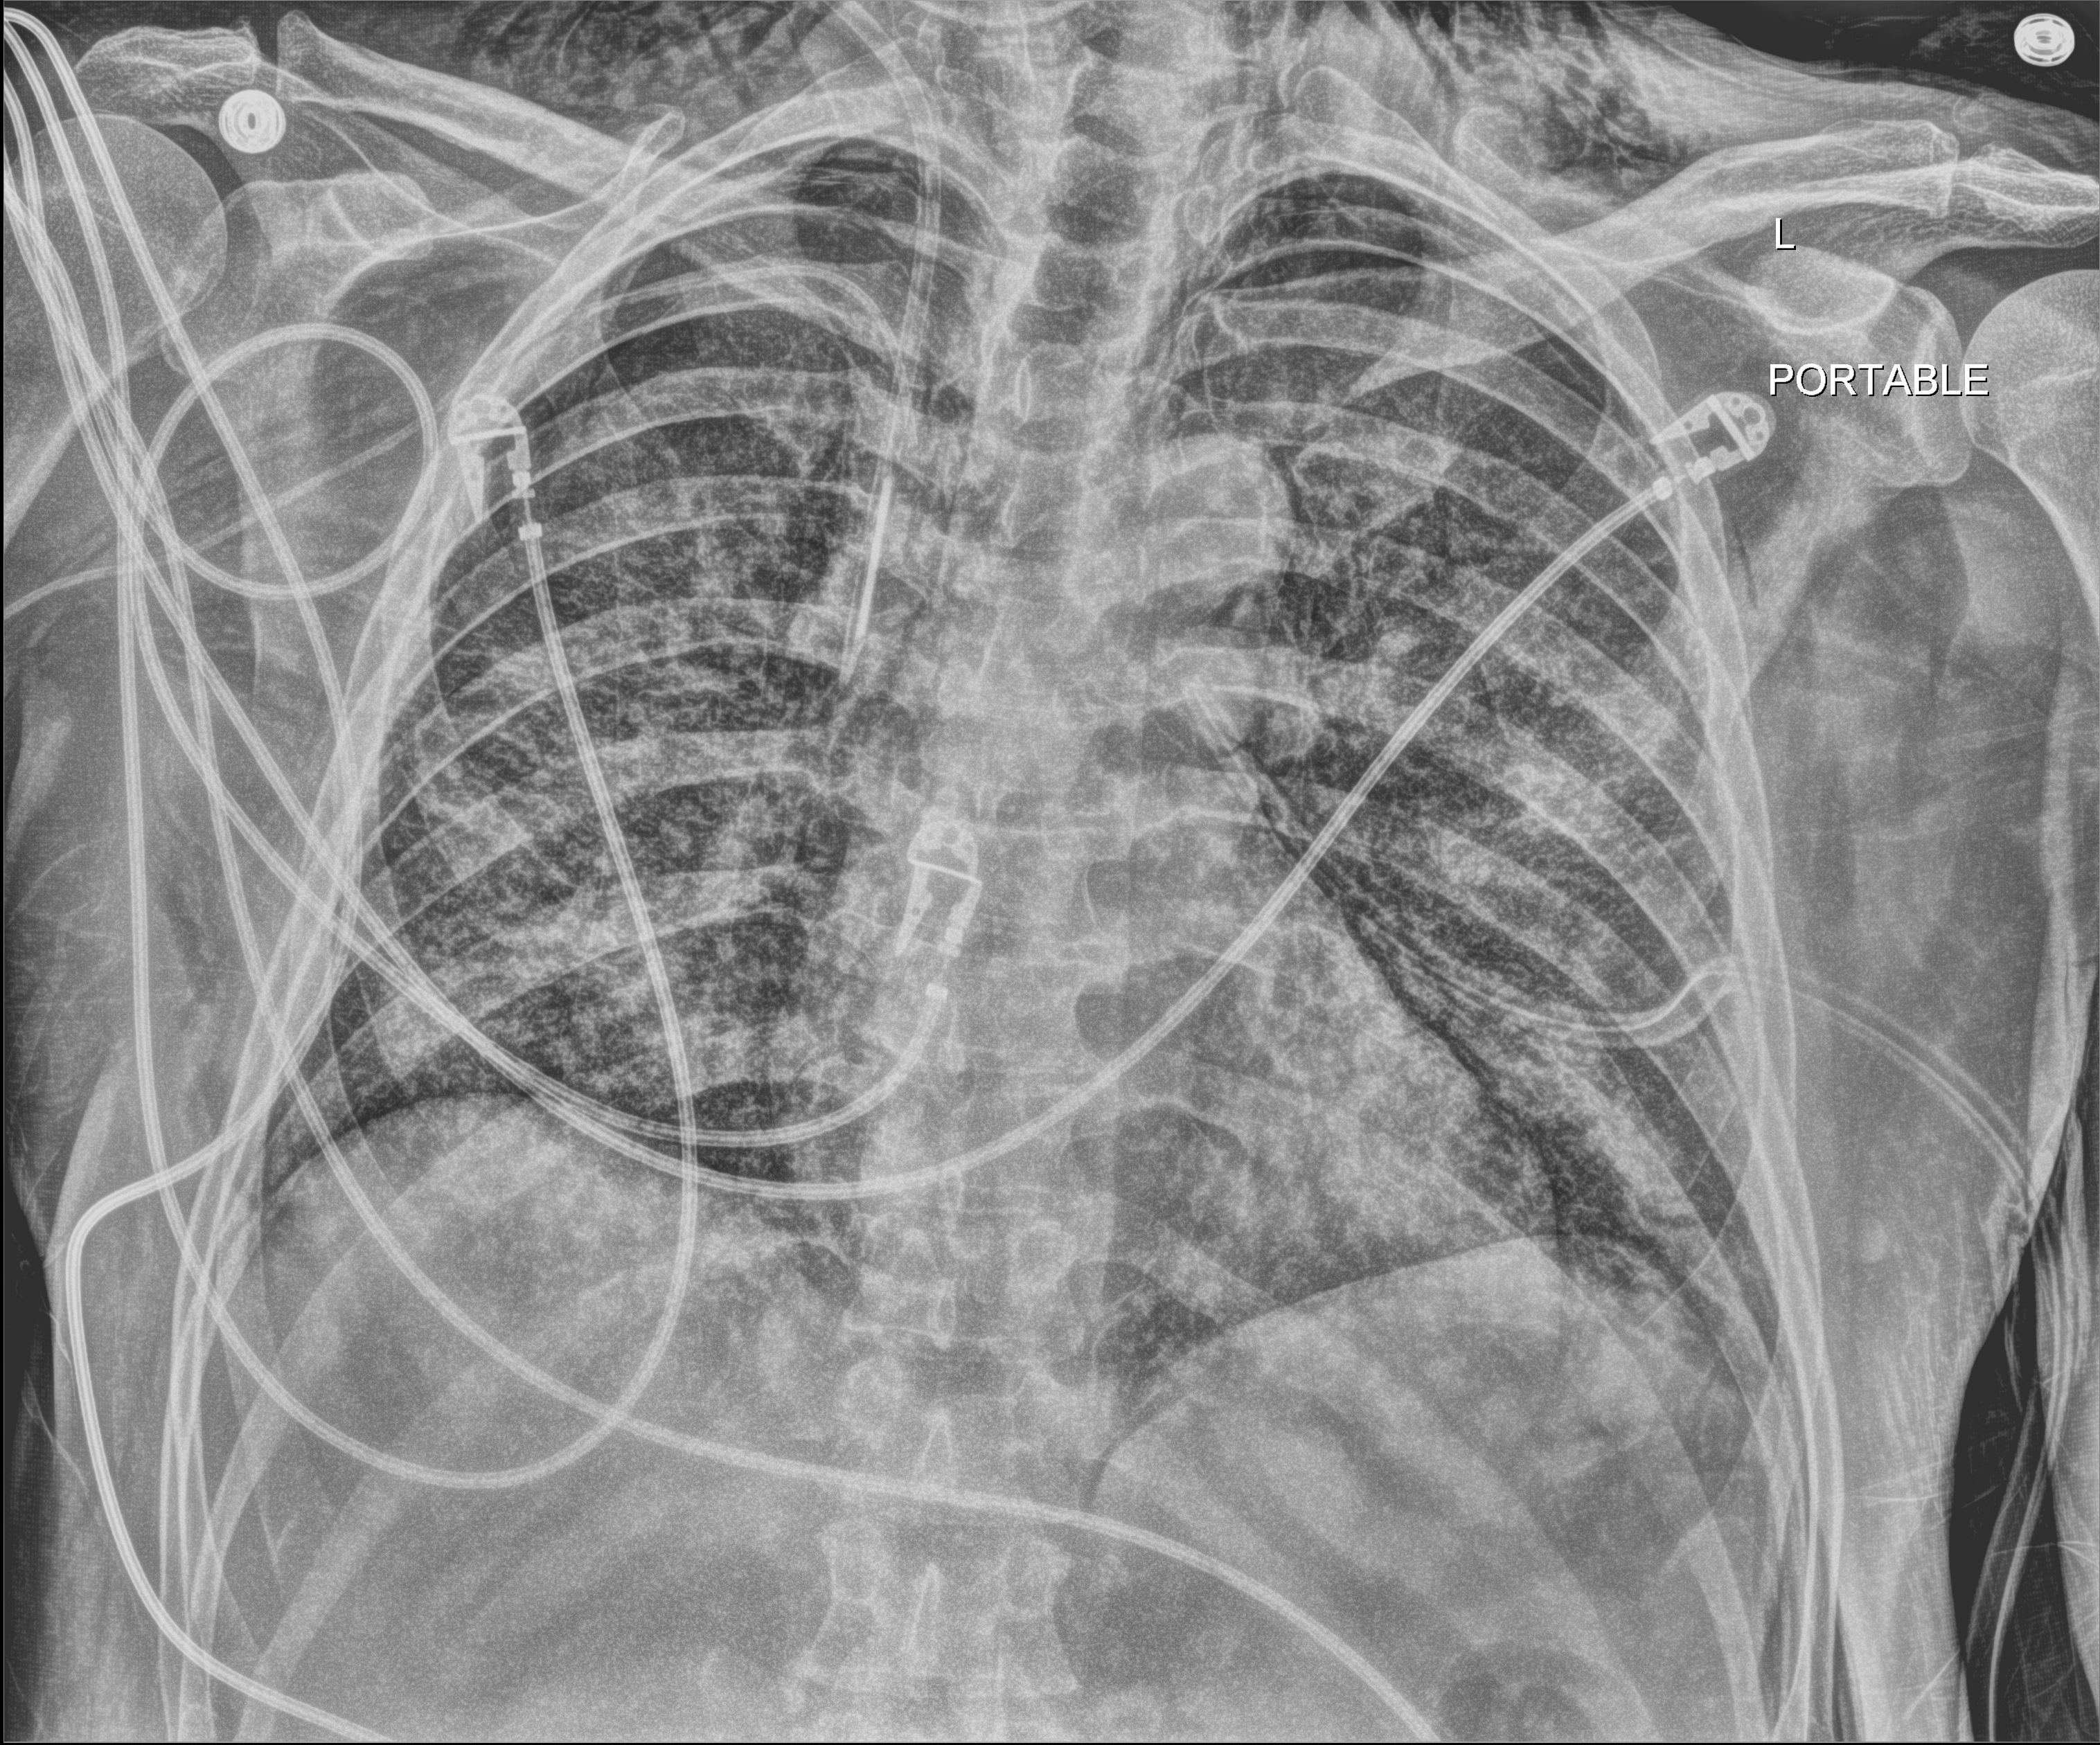
Bedside chest radiograph (digital radiography), anteroposterior (AP) projection. Patient hospitalised with COVID-19; male, aged 18–59 years.
Admission-level facts for this patient (not findings on this image; timing relative to this image not recorded): admitted to intensive care during this hospital stay: yes; diabetes (admission record): no.